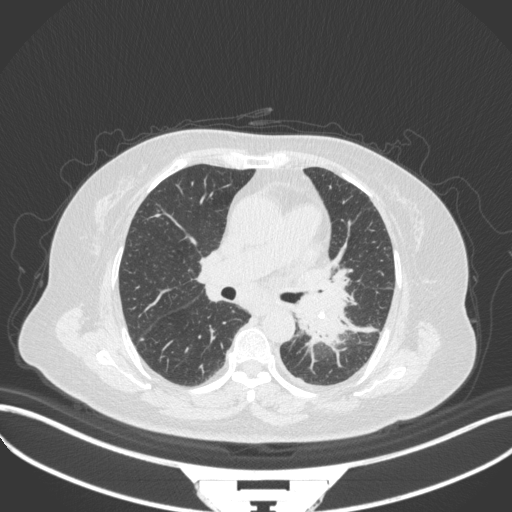
Chest CT, one axial slice. Slice 198 of 328 in the series (ordered by position). Lung window (W 1500 / L -600 HU). 512 × 512 image matrix, field of view 400 × 400 mm. Patient: female, 69 years. From the clinical record (not read from this slice): clinical TNM (as recorded): T2b N3 M1.
Structures marked on this image (bounding box drawn by a radiologist):
- lung tumour (recorded histology: adenocarcinoma): box from (x=294, y=284) to (x=351, y=349) px